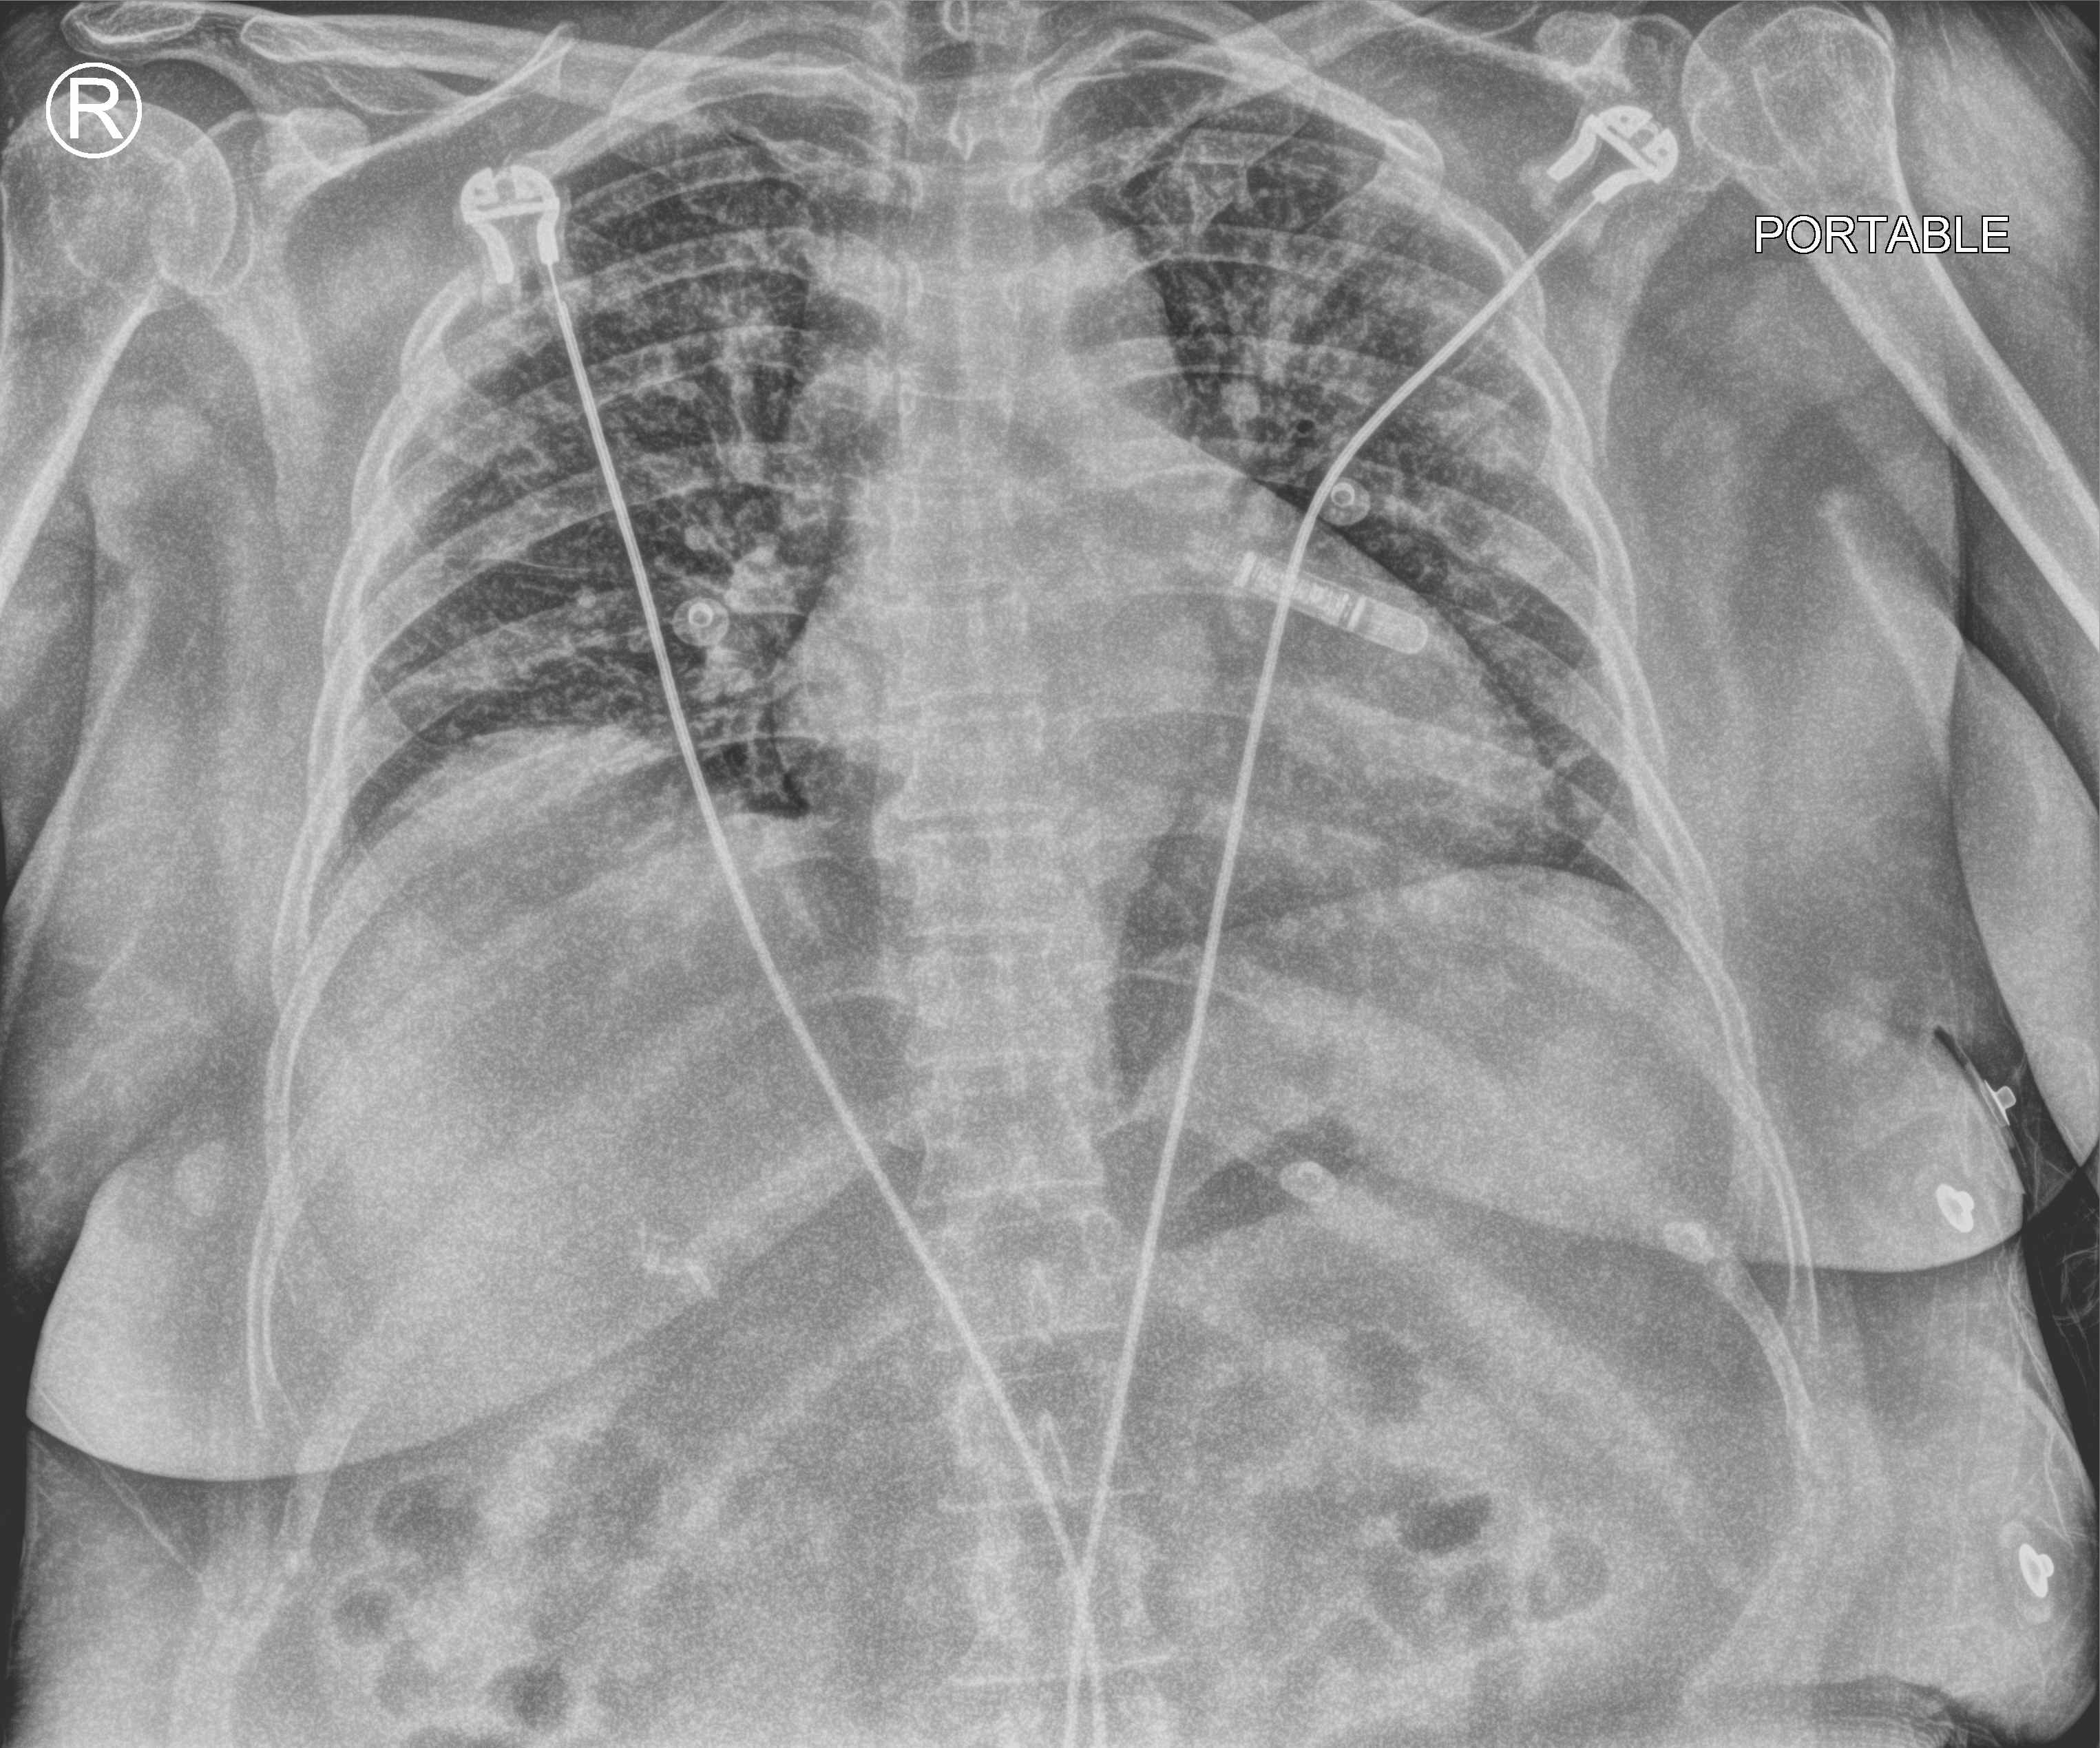
Chest X-ray (portable), anteroposterior (AP) projection. Female patient hospitalised with COVID-19, age 18–59 years.
Hospital-stay facts (about this admission, not read from this image; timing relative to this image not recorded): mechanically ventilated during this hospital stay: no.